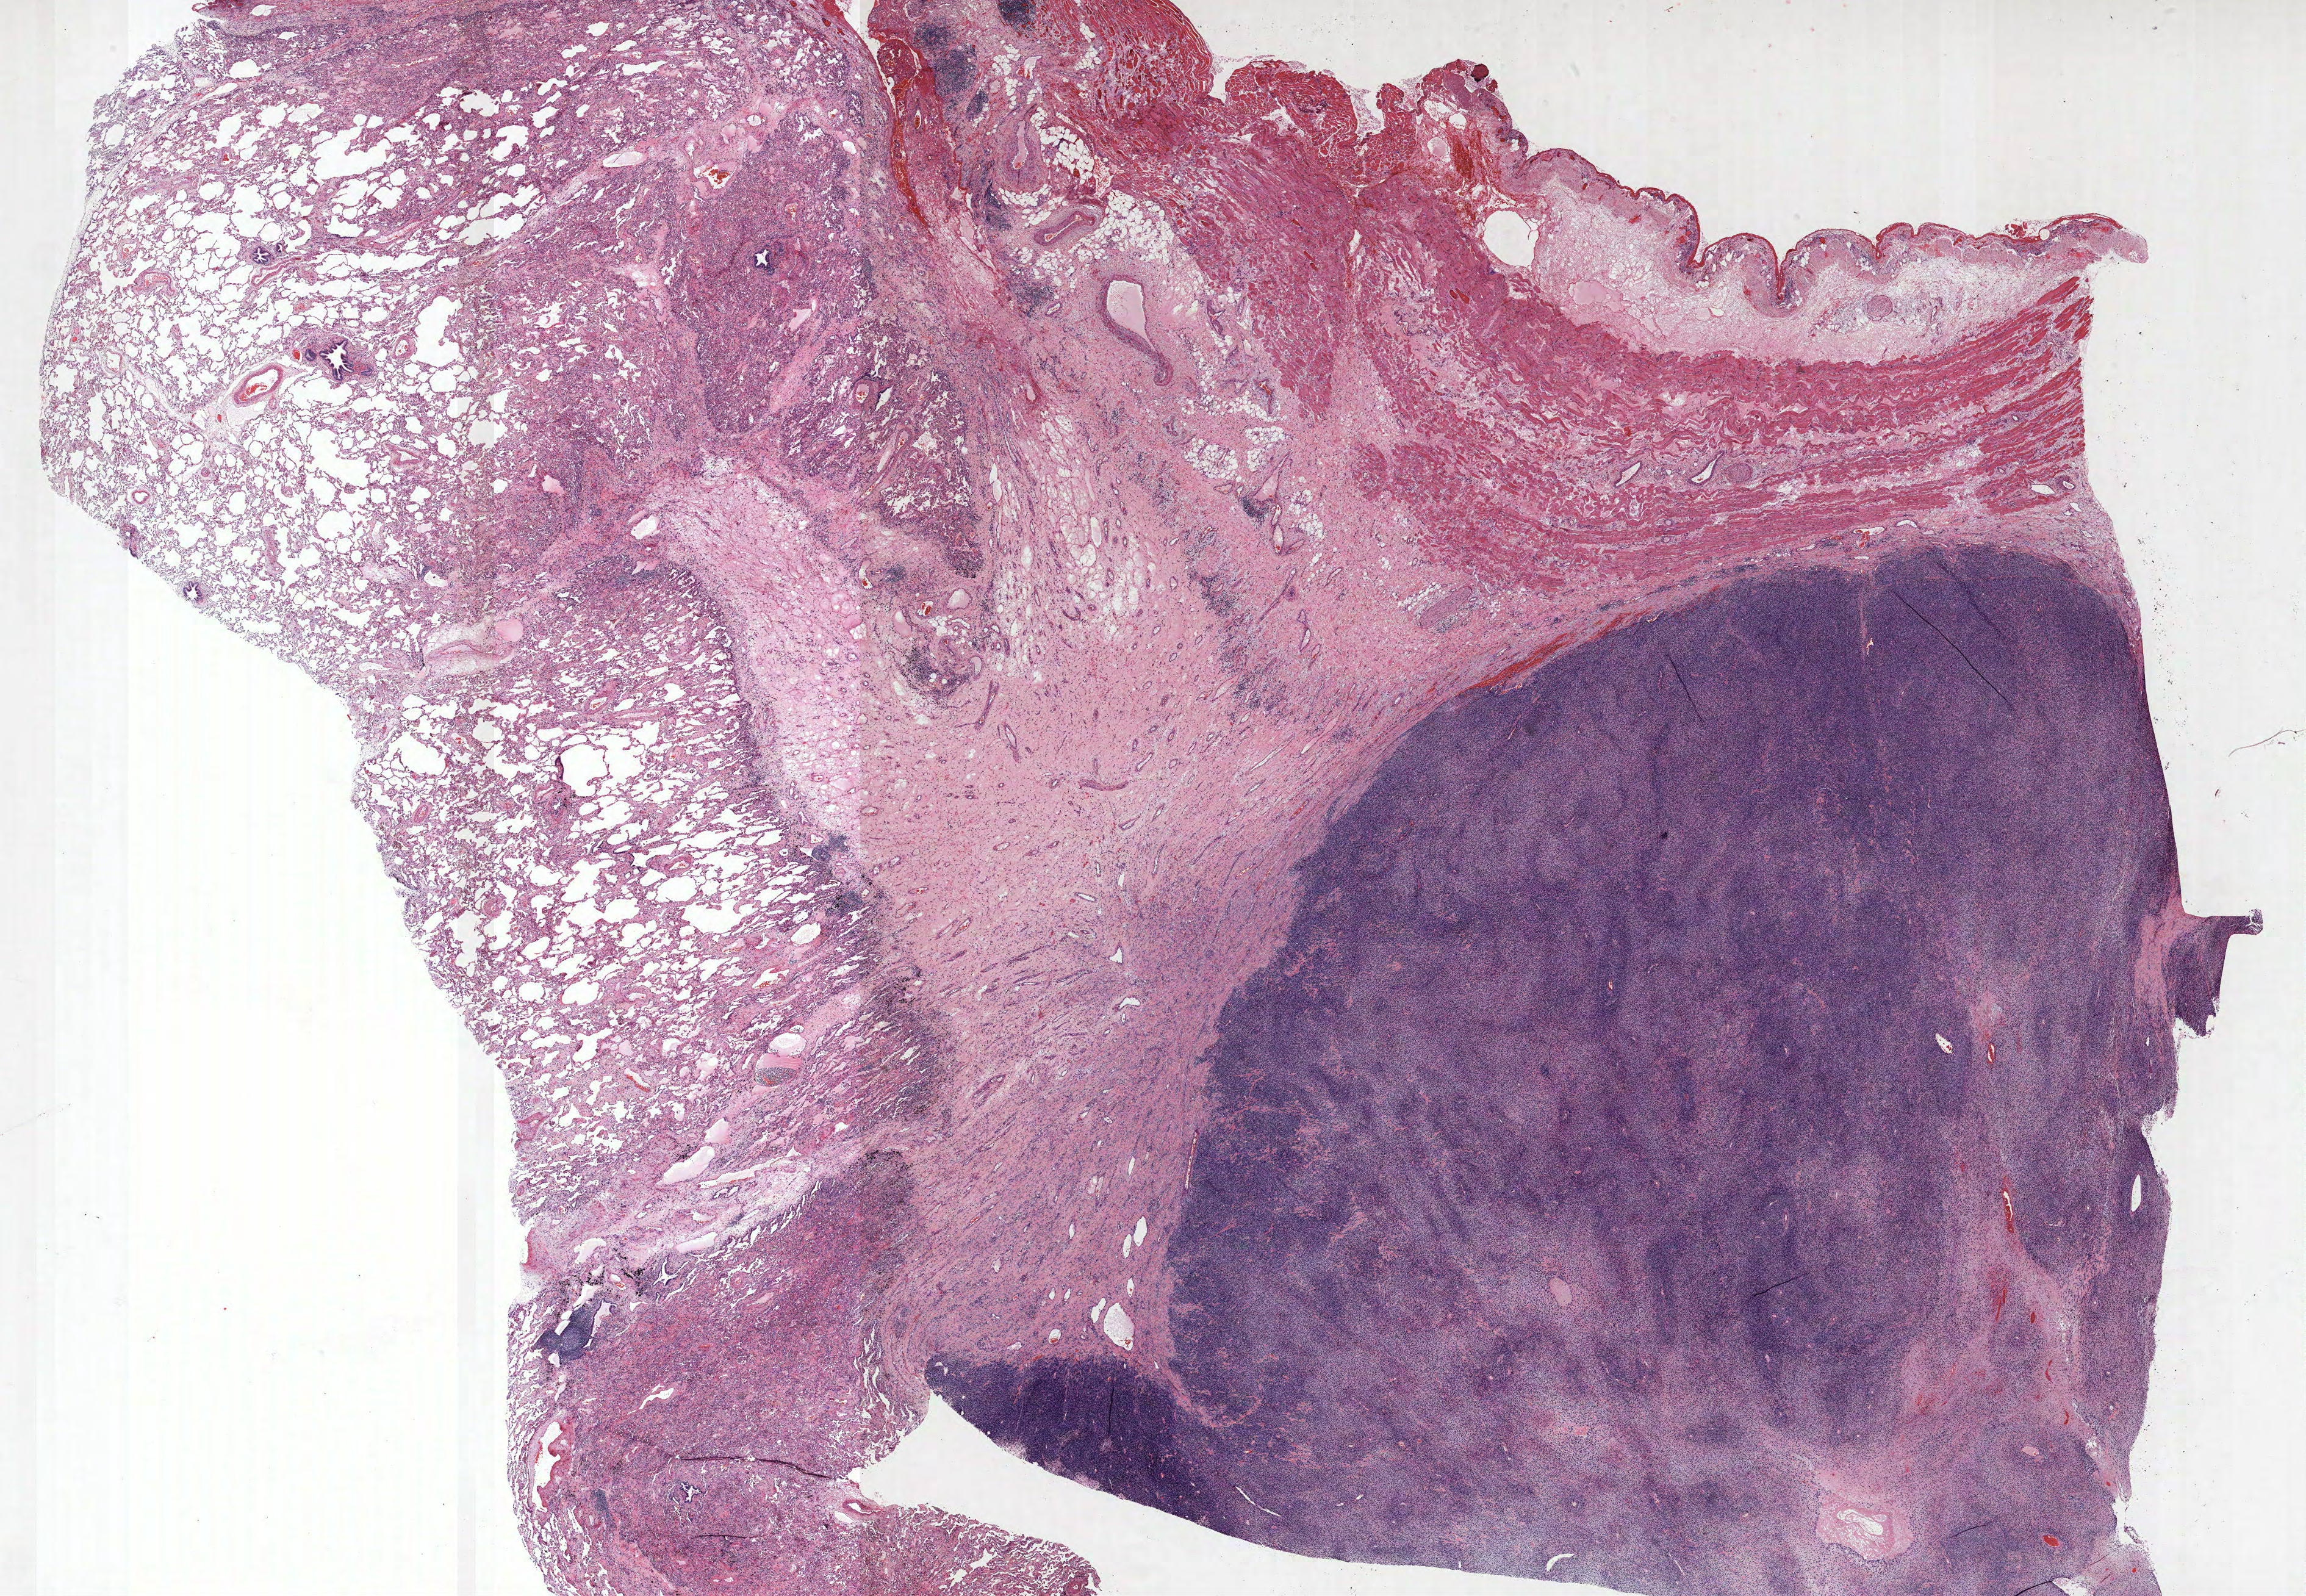
H&E-stained whole-slide image — shown as a low-resolution overview of the whole scanned area (about 30.2 x 20.9 mm); formalin-fixed paraffin-embedded (FFPE) section; lung tissue. Female, age 67 at enrolment. Current smoker at enrolment. Grade: undifferentiated (G4).
Participant's lung-cancer diagnosis: Pseudosarcomatous carcinoma (ICD-O-3 8033/3). Primary tumour location (clinical record): right lower lobe. Stage (AJCC 6th edition): IIIB. Tumour size (pathology): 135 mm.